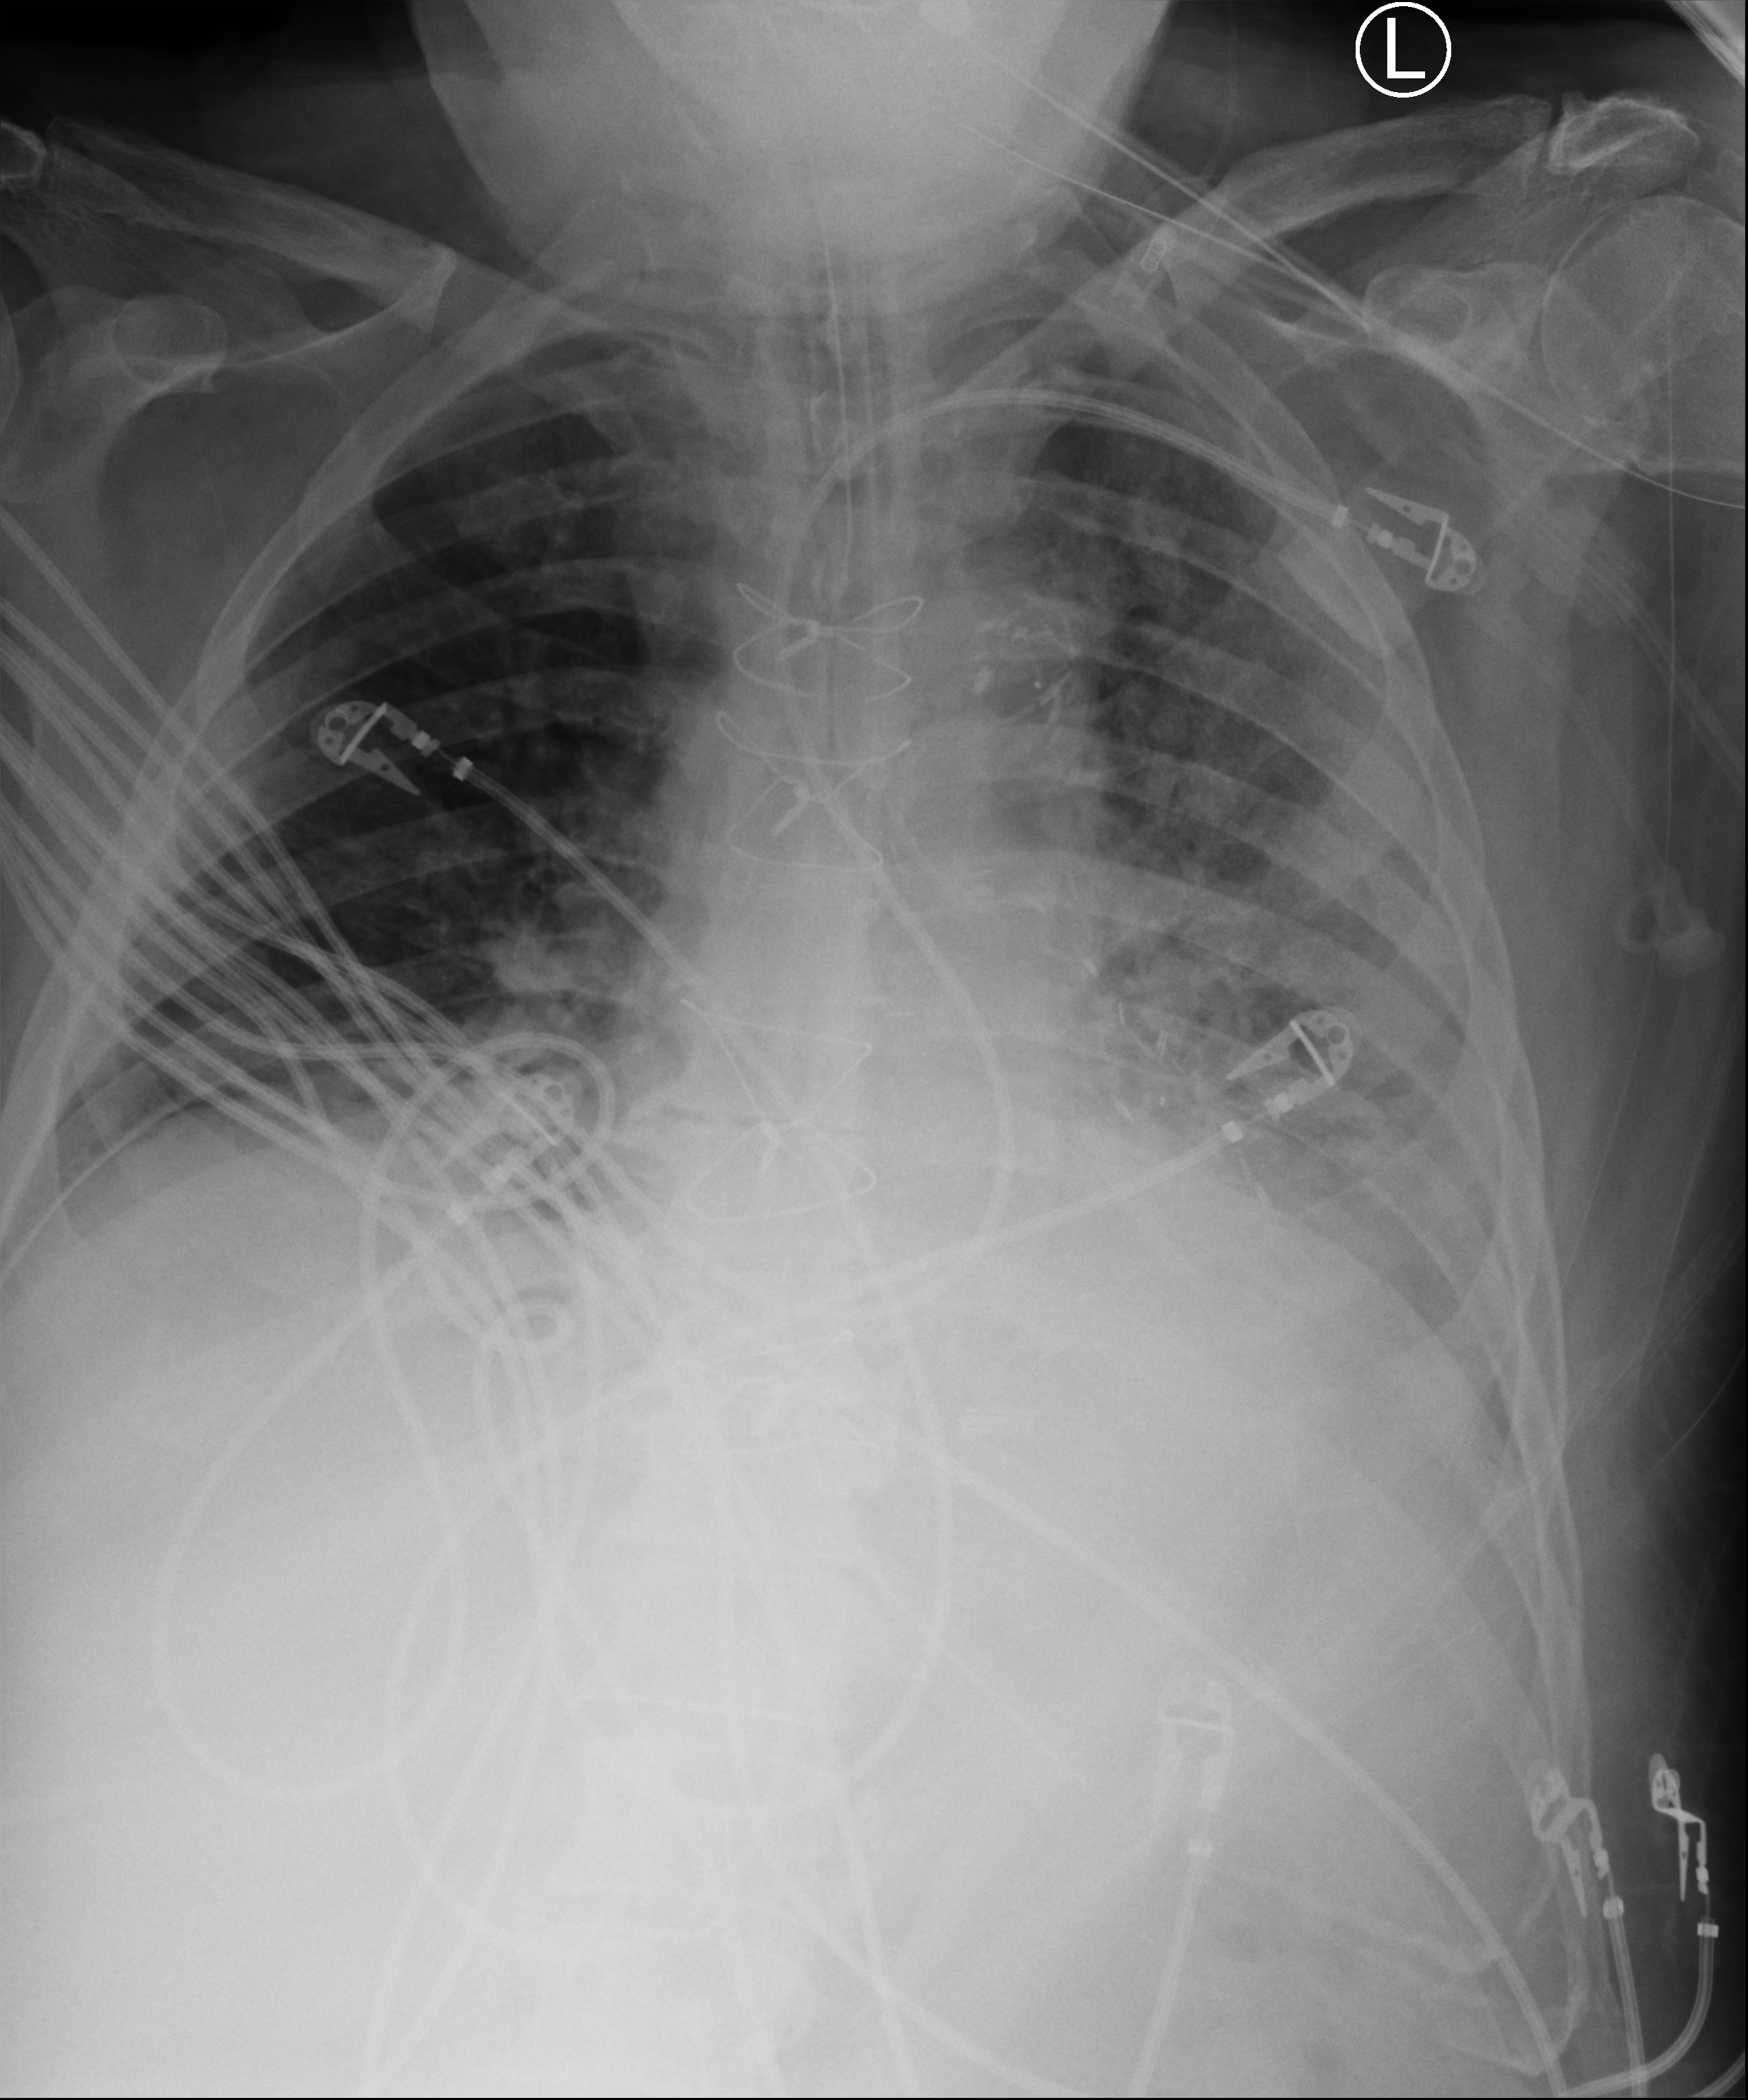
Bedside chest radiograph (computed radiography), anteroposterior (AP) projection. Male patient hospitalised with COVID-19, age 60–74 years.
Admission-level facts for this patient (not findings on this image; timing relative to this image not recorded): admitted to intensive care during this hospital stay: yes; smoking status (admission record): former; mechanically ventilated during this hospital stay: yes.